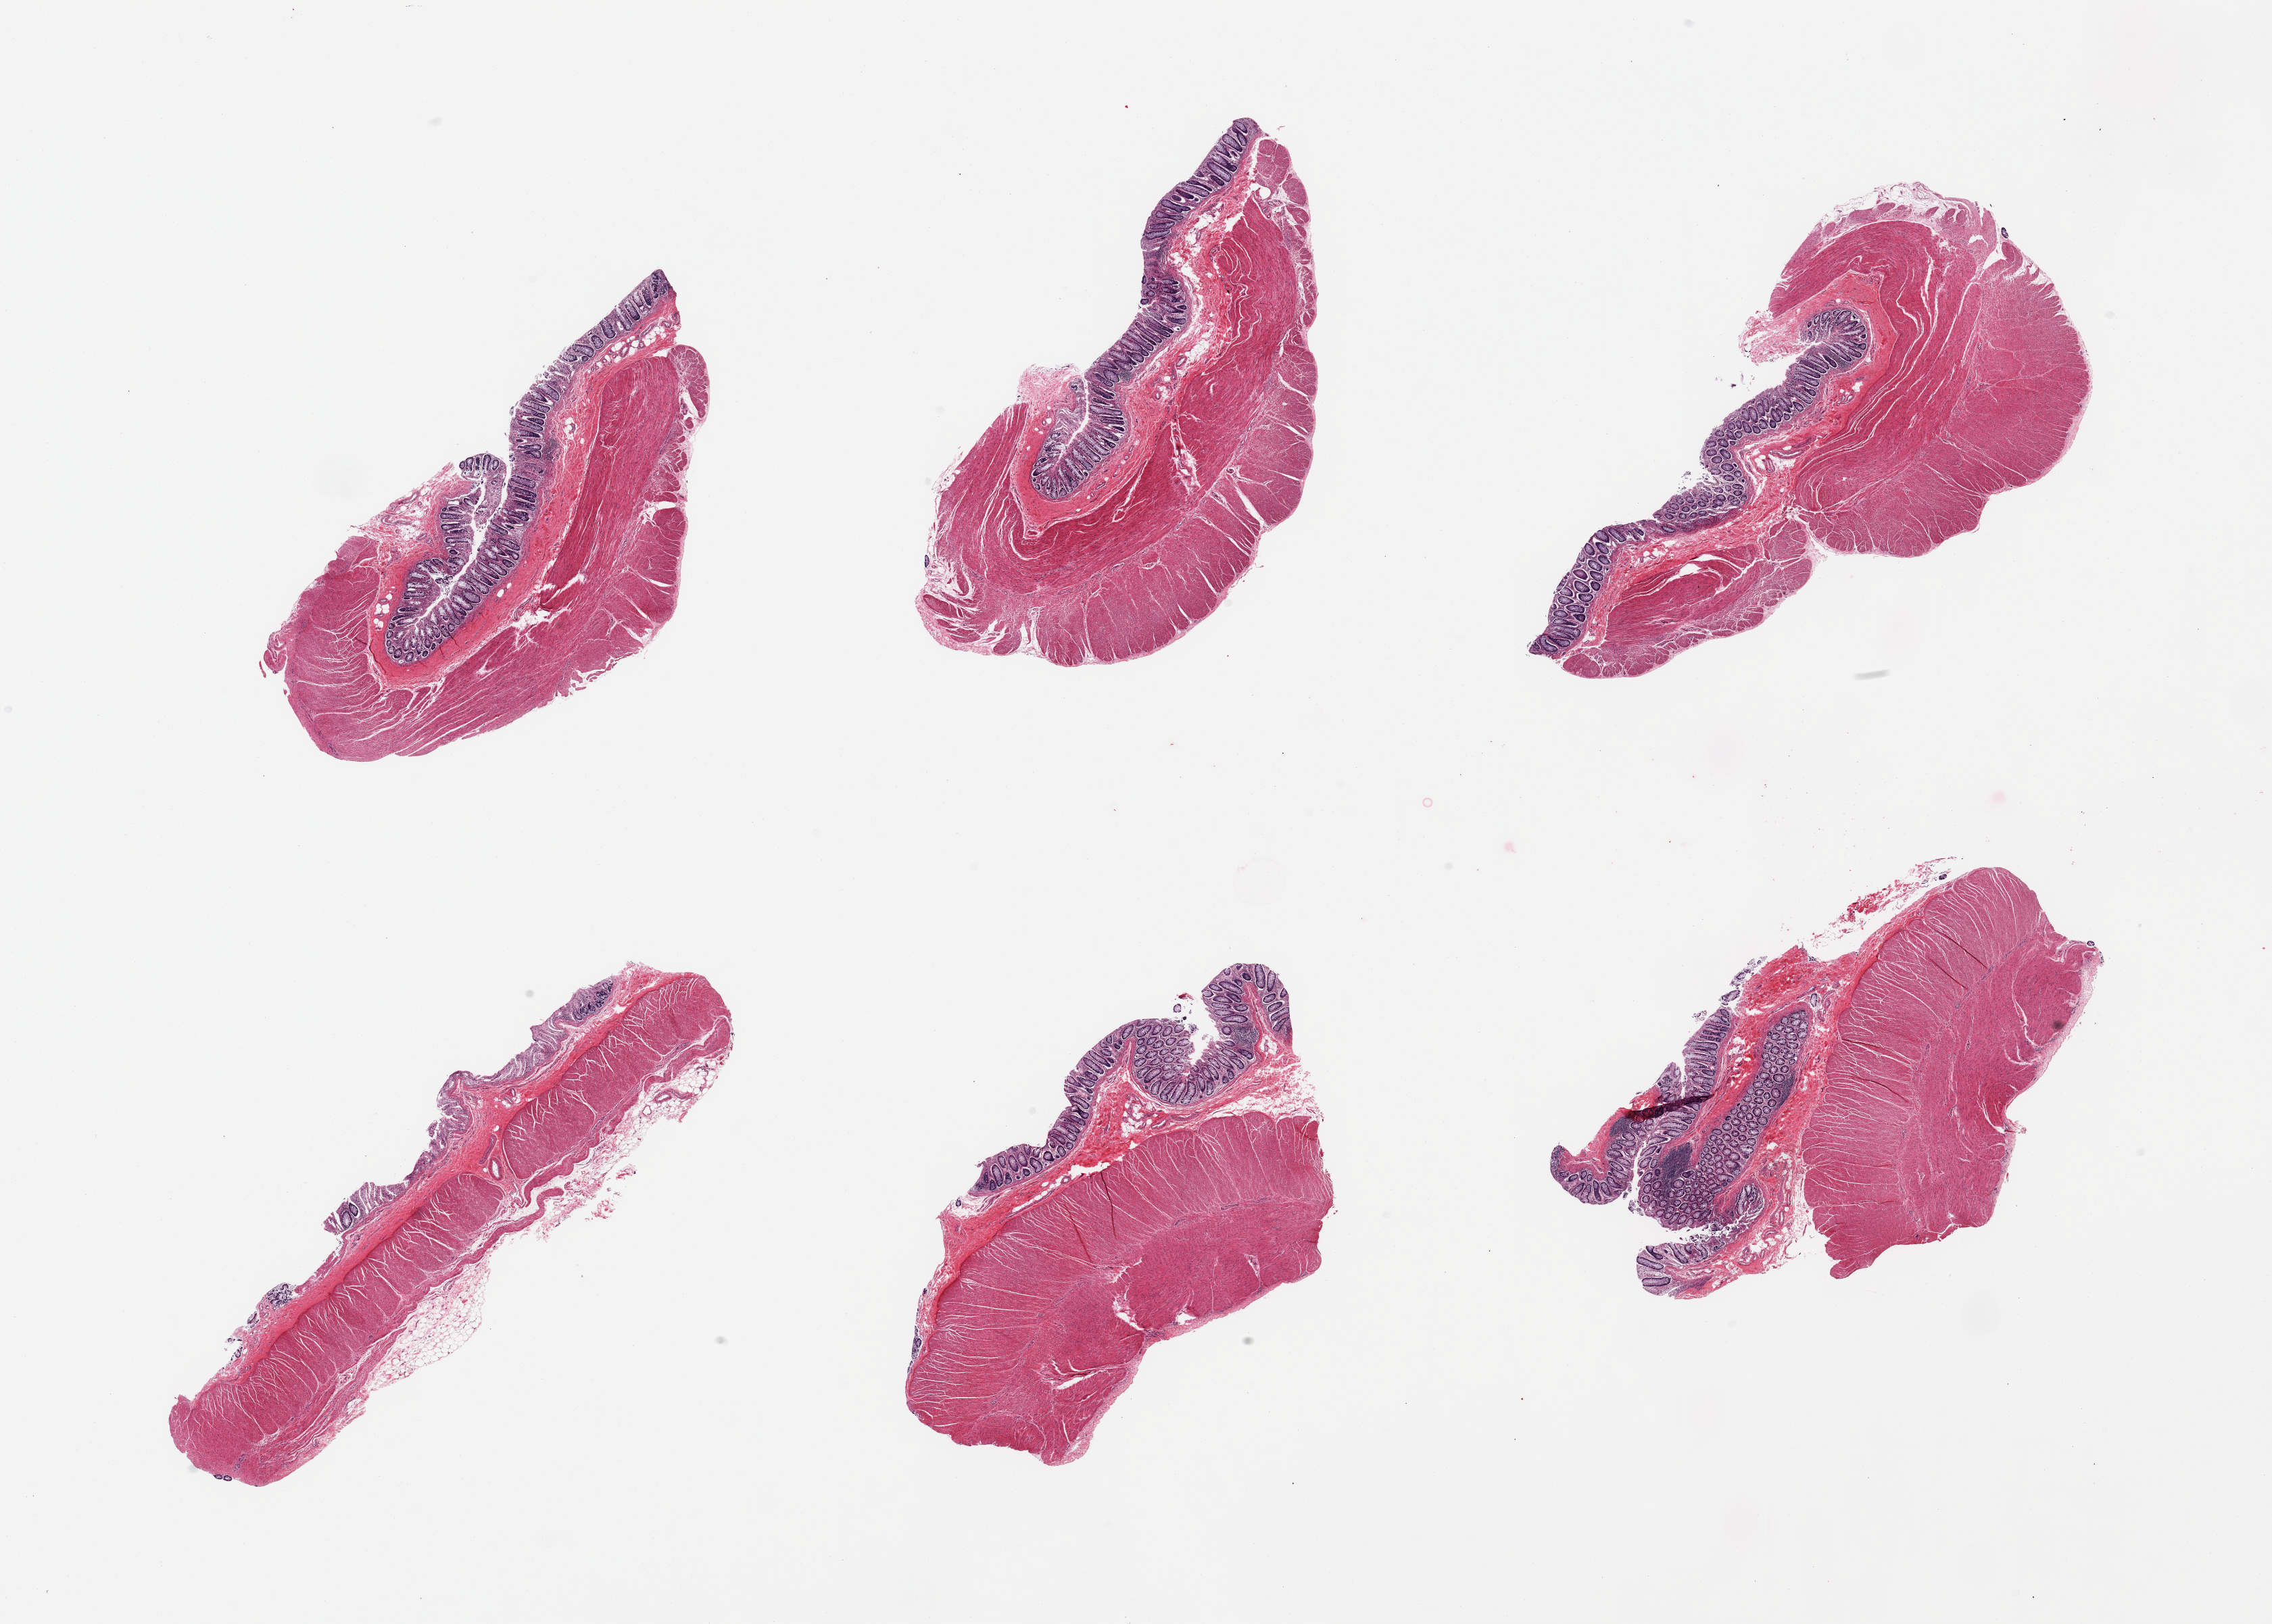
Whole-slide image, haematoxylin and eosin stain, brightfield, a low-resolution overview of the entire scanned area, about 26.6 x 19.0 mm (acquisition: 20x scan); PAXgene-fixed paraffin-embedded (PFPE) section; sampled site (target tissue): sigmoid colon; tissue donor sample. Donor sex: female.
• review note (as recorded): 6 pieces; mildly autolyzed mucosa (not target) and well preserved muscularis (target)